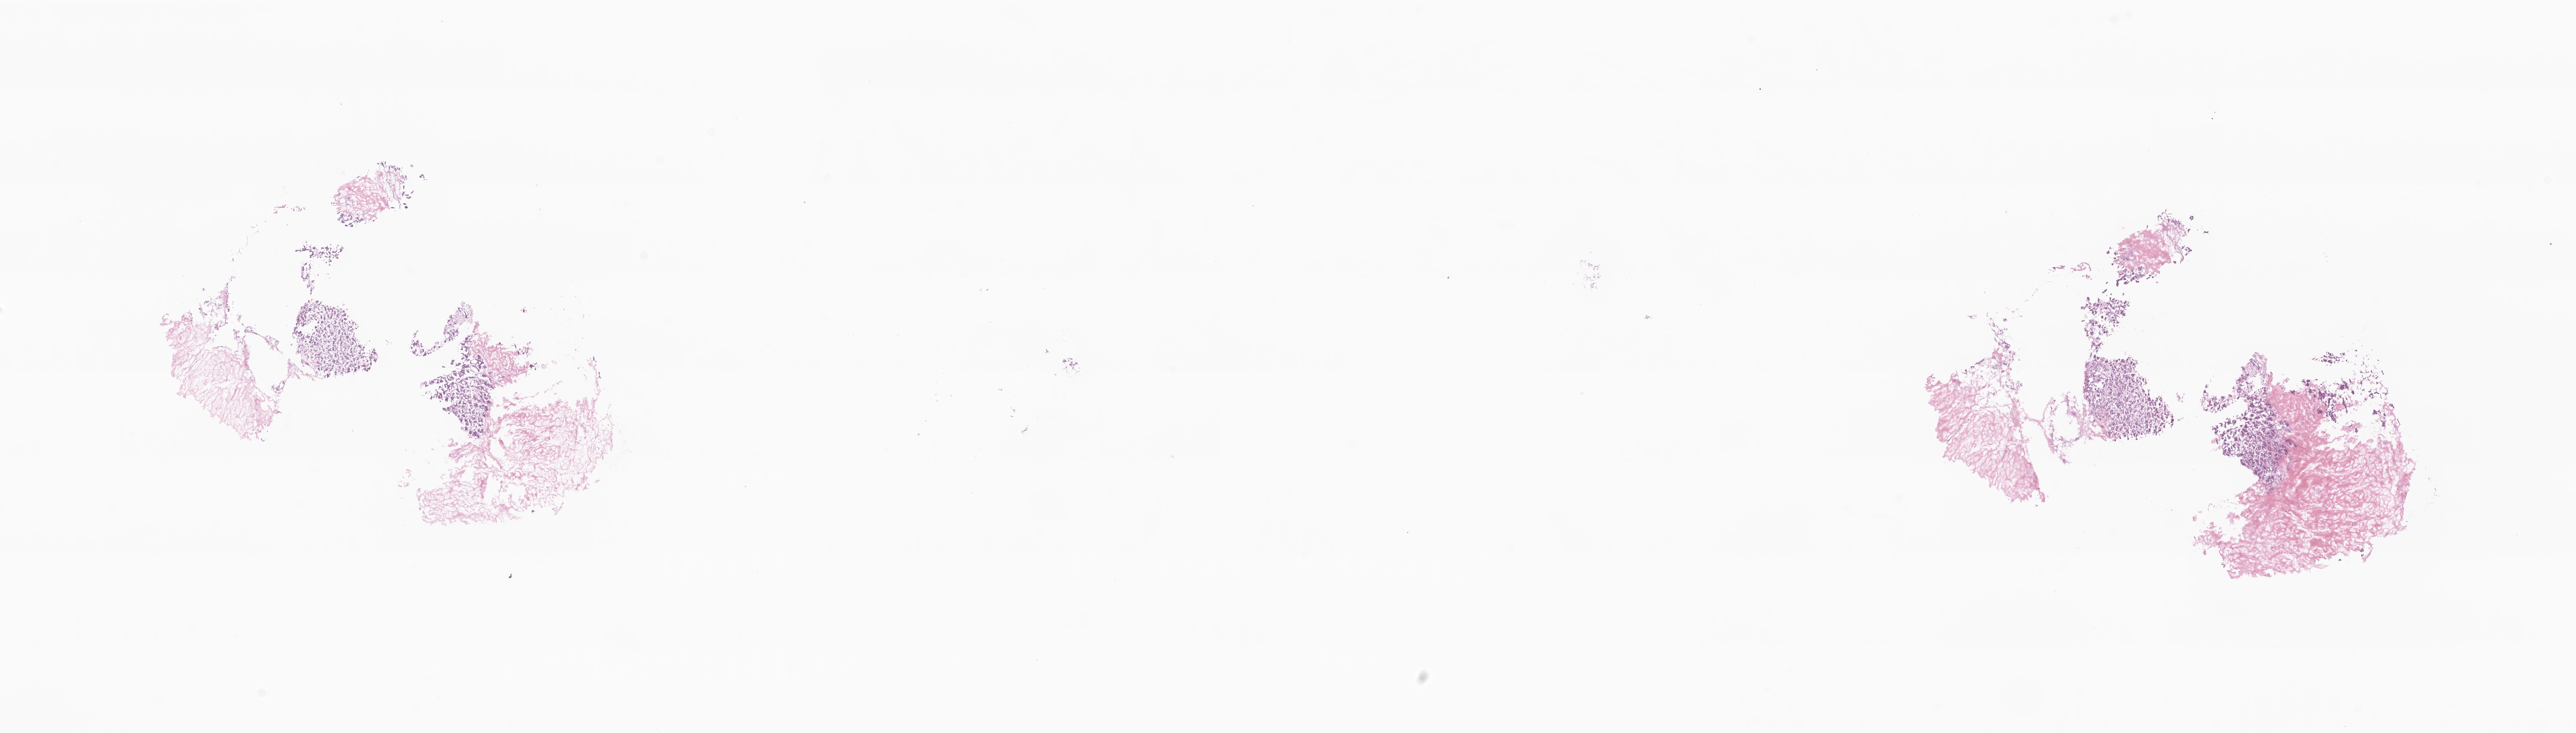
H&E whole-slide image — low-resolution overview of the scanned area, about 29.9 x 8.5 mm, frozen section (tissue freezing medium), specimen: primary tumor, anatomic site: breast (right). Patient: female, age at initial diagnosis 61 years. Composition of this section per pathologist review: tumor cells 30%, tumor nuclei 95%, stromal cells 70%, necrosis 0%, normal cells 0%. Infiltration values recorded for this section: lymphocyte infiltration 0%, monocyte infiltration 0%, neutrophil infiltration 0%.
* section: top of the tissue portion
* diagnosis: Infiltrating duct carcinoma, NOS